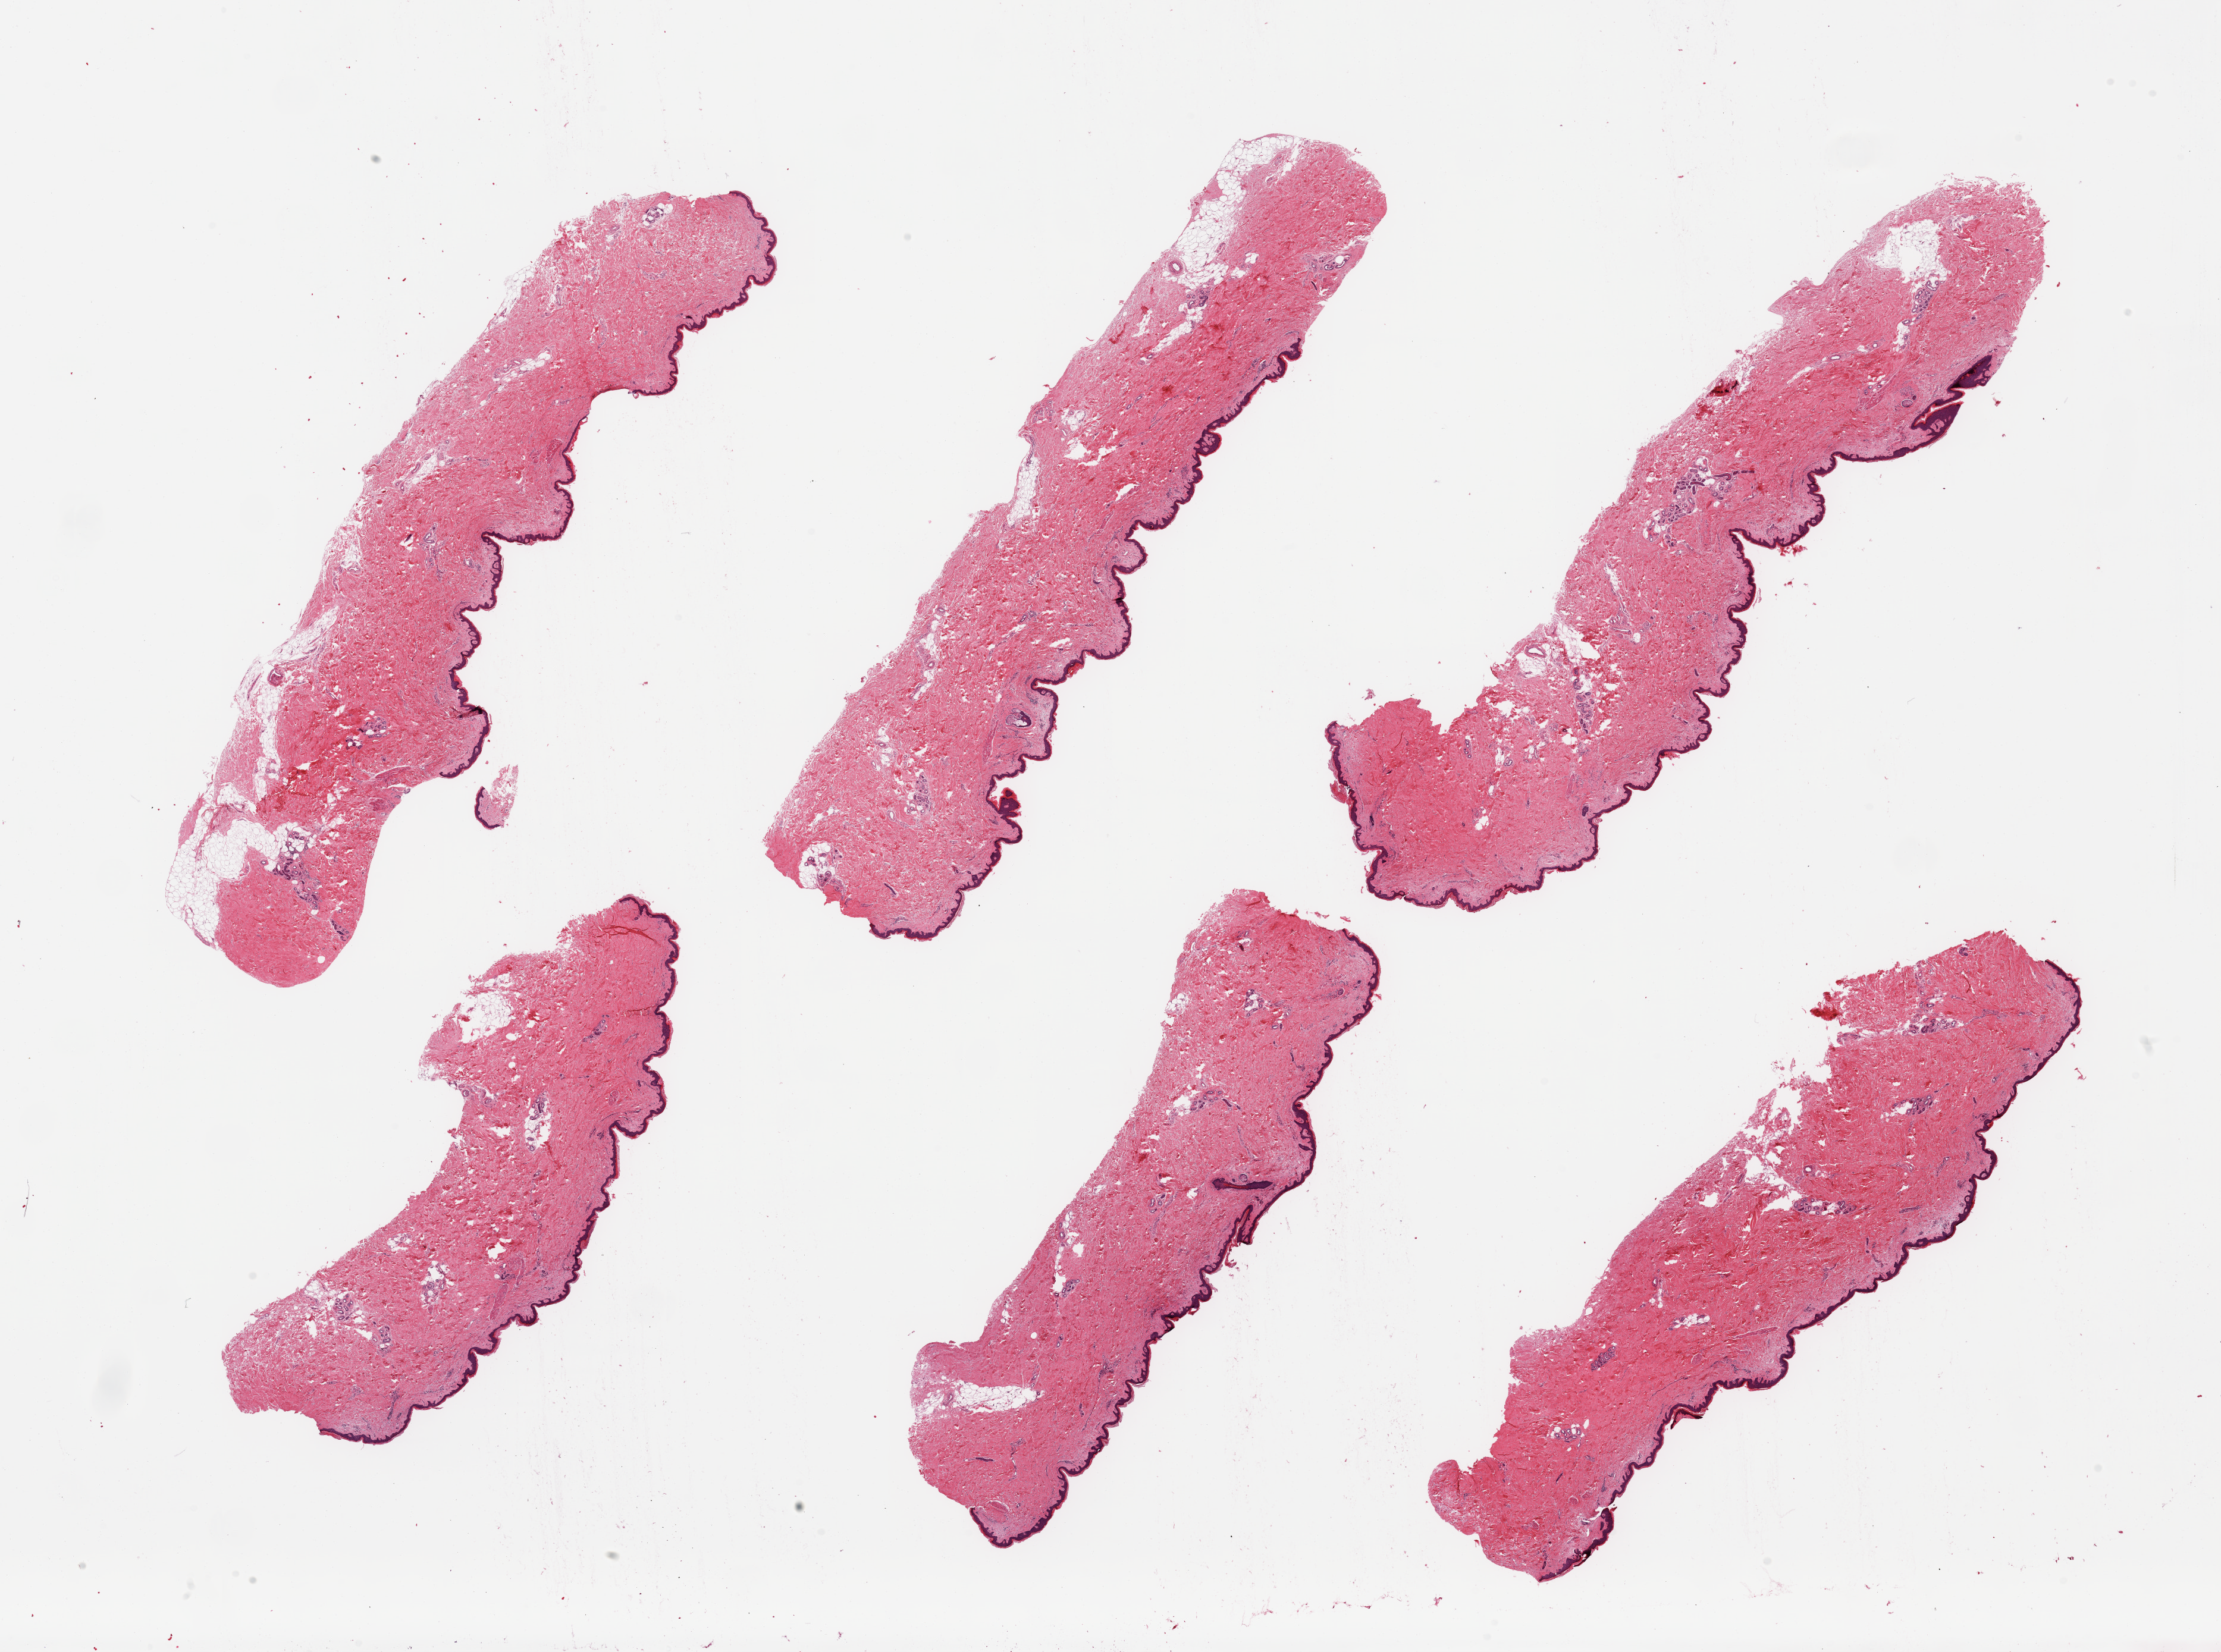
Whole-slide image, H&E stain, brightfield — a low-resolution overview of the entire scanned area, about 29.5 x 22.0 mm (from a 20x scan). PAXgene-fixed paraffin-embedded (PFPE) section. Target tissue: skin of lower leg. Tissue donor sample. Male donor.
Review note (as recorded): 6 pieces; well trimmed; 5% dermal fat.